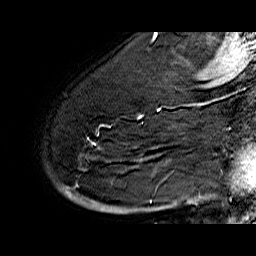
Breast MRI (dynamic contrast-enhanced), one sagittal slice. Position 46 of 60 along the scan axis. Dynamic contrast-enhanced series, time point 2 of 6 at this slice position (early post-contrast). 1.5 T. TE 6.4 ms, TR 32.9 ms. 4 mm slice thickness. 256 × 256 image matrix, field of view 200 × 200 mm. Female patient. Case-level facts recorded for this patient, not image findings: setting: breast cancer imaged before/during neoadjuvant chemotherapy; receptor status: HR-positive, HER2-negative.
Structures marked on this image (semi-automatically segmented with operator editing):
- analysis volume of interest (the breast-tissue region the enhancement analysis was run in; not a lesion): bounding box (x1, y1, x2, y2) in pixels: (54, 74, 176, 210)
- tumour enhancement mask (voxels above the 100 % enhancement threshold inside the analysis volume of interest): (65, 108, 159, 204)